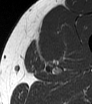
MRI of an extremity soft-tissue mass, one axial slice; slice 43 of 62 in the series (ordered by position); MR volume resampled by the dataset authors to the PET/CT grid (not the native acquisition matrix); 3.27 mm slice thickness; 92 × 104 image matrix, field of view 90 × 102 mm. Male patient. Case-level facts recorded for this patient, not image findings: histological type: mixoid liposarcoma; grade: low; site of the primary tumour: left thigh.
Annotated regions visible in this slice (expert contour drawn on MRI and transferred to this co-registered scan by the dataset authors):
- gross tumour volume (mass): bounding box <37,37,65,64> (left, top, right, bottom; pixels)